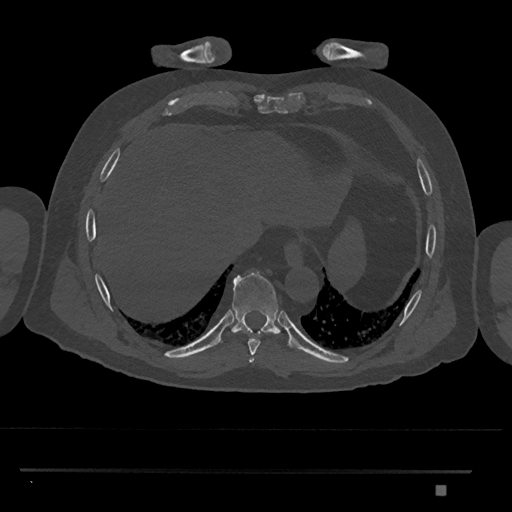
CT including the spine, one axial slice; position 1077 of 1134 along the scan axis; reconstruction kernel Br40s/3; 120 kVp; bone window (W 1800 / L 400 HU); 0.5 mm slice thickness; 512 × 512 image matrix, field of view 429 × 429 mm. Male patient, age 65 years. From the clinical record (not read from this slice): primary cancer: prostate.
Outlined on this slice (semi-automatic segmentation, software-assisted and operator-edited):
- T8 vertebra: bounding box (x1, y1, x2, y2) in pixels: (248, 339, 260, 355)
- T9 vertebra: (217, 270, 291, 347)